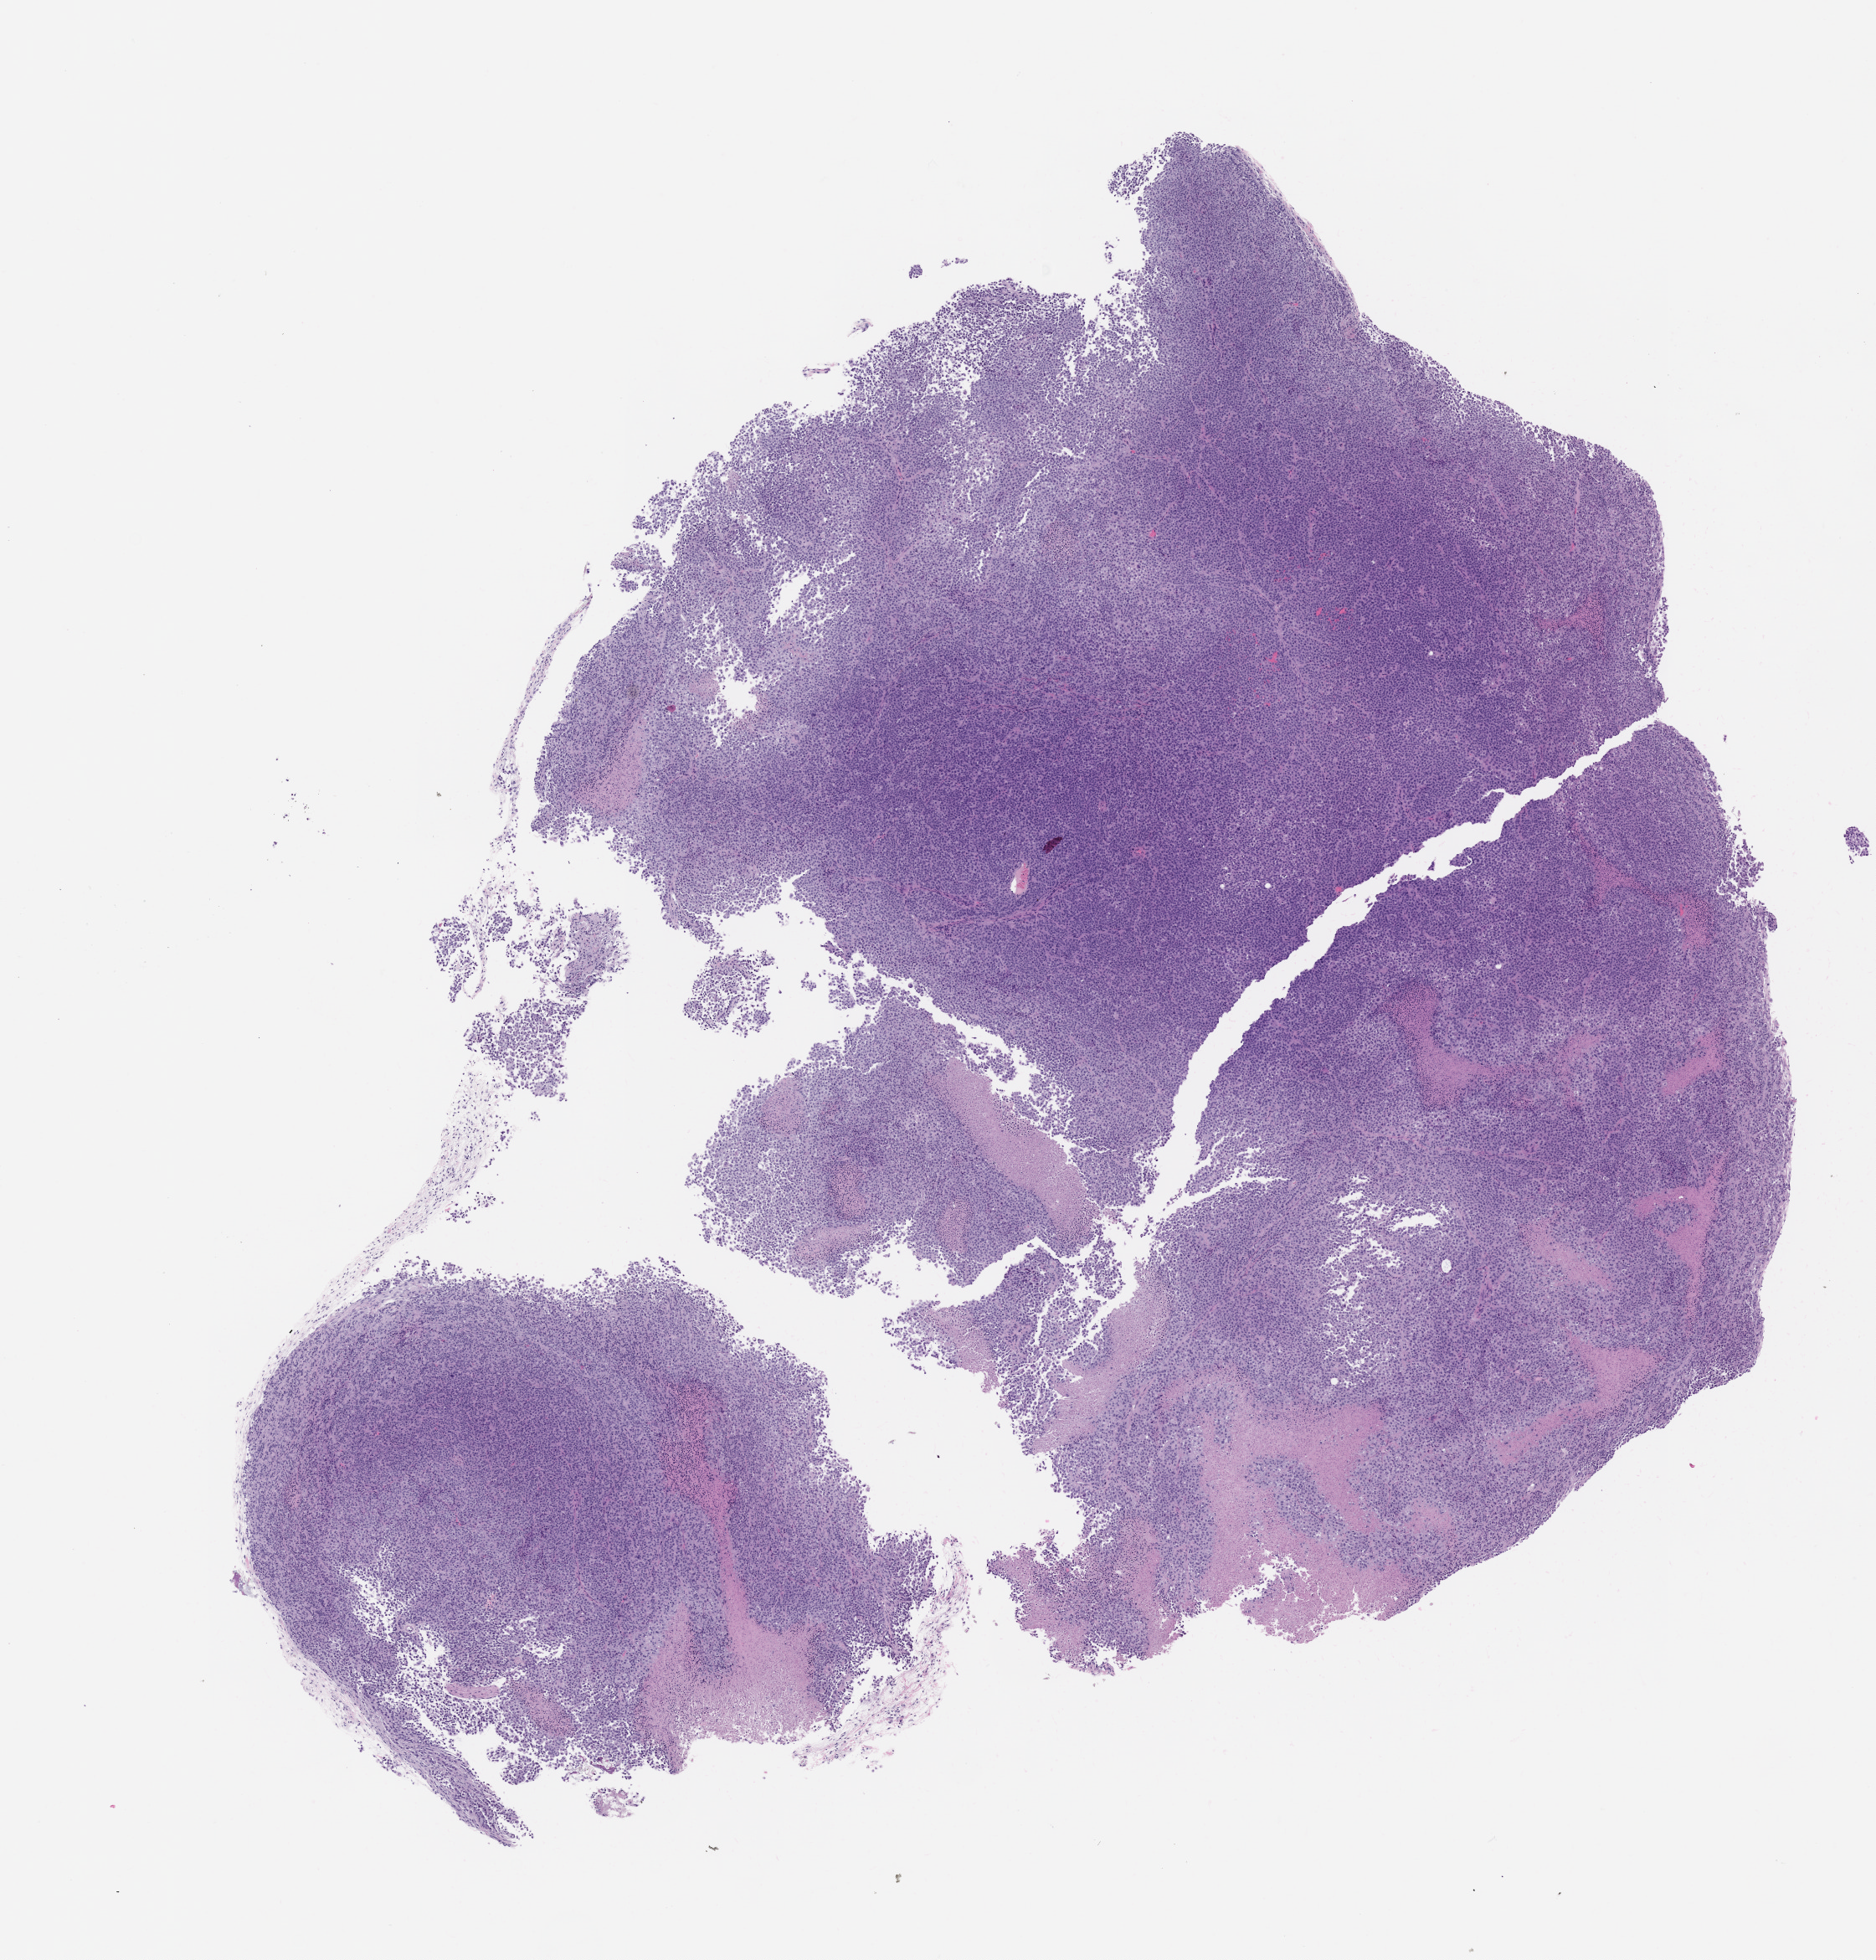
Whole-slide image, haematoxylin and eosin: patient-derived xenograft (human tumor grown in a mouse), passage 2 — whole scanned area (about 9.0 x 9.4 mm) shown as a low-resolution overview, formalin-fixed, paraffin-embedded (FFPE) tissue.
Originating patient diagnosis: Mesothelial Neoplasm.